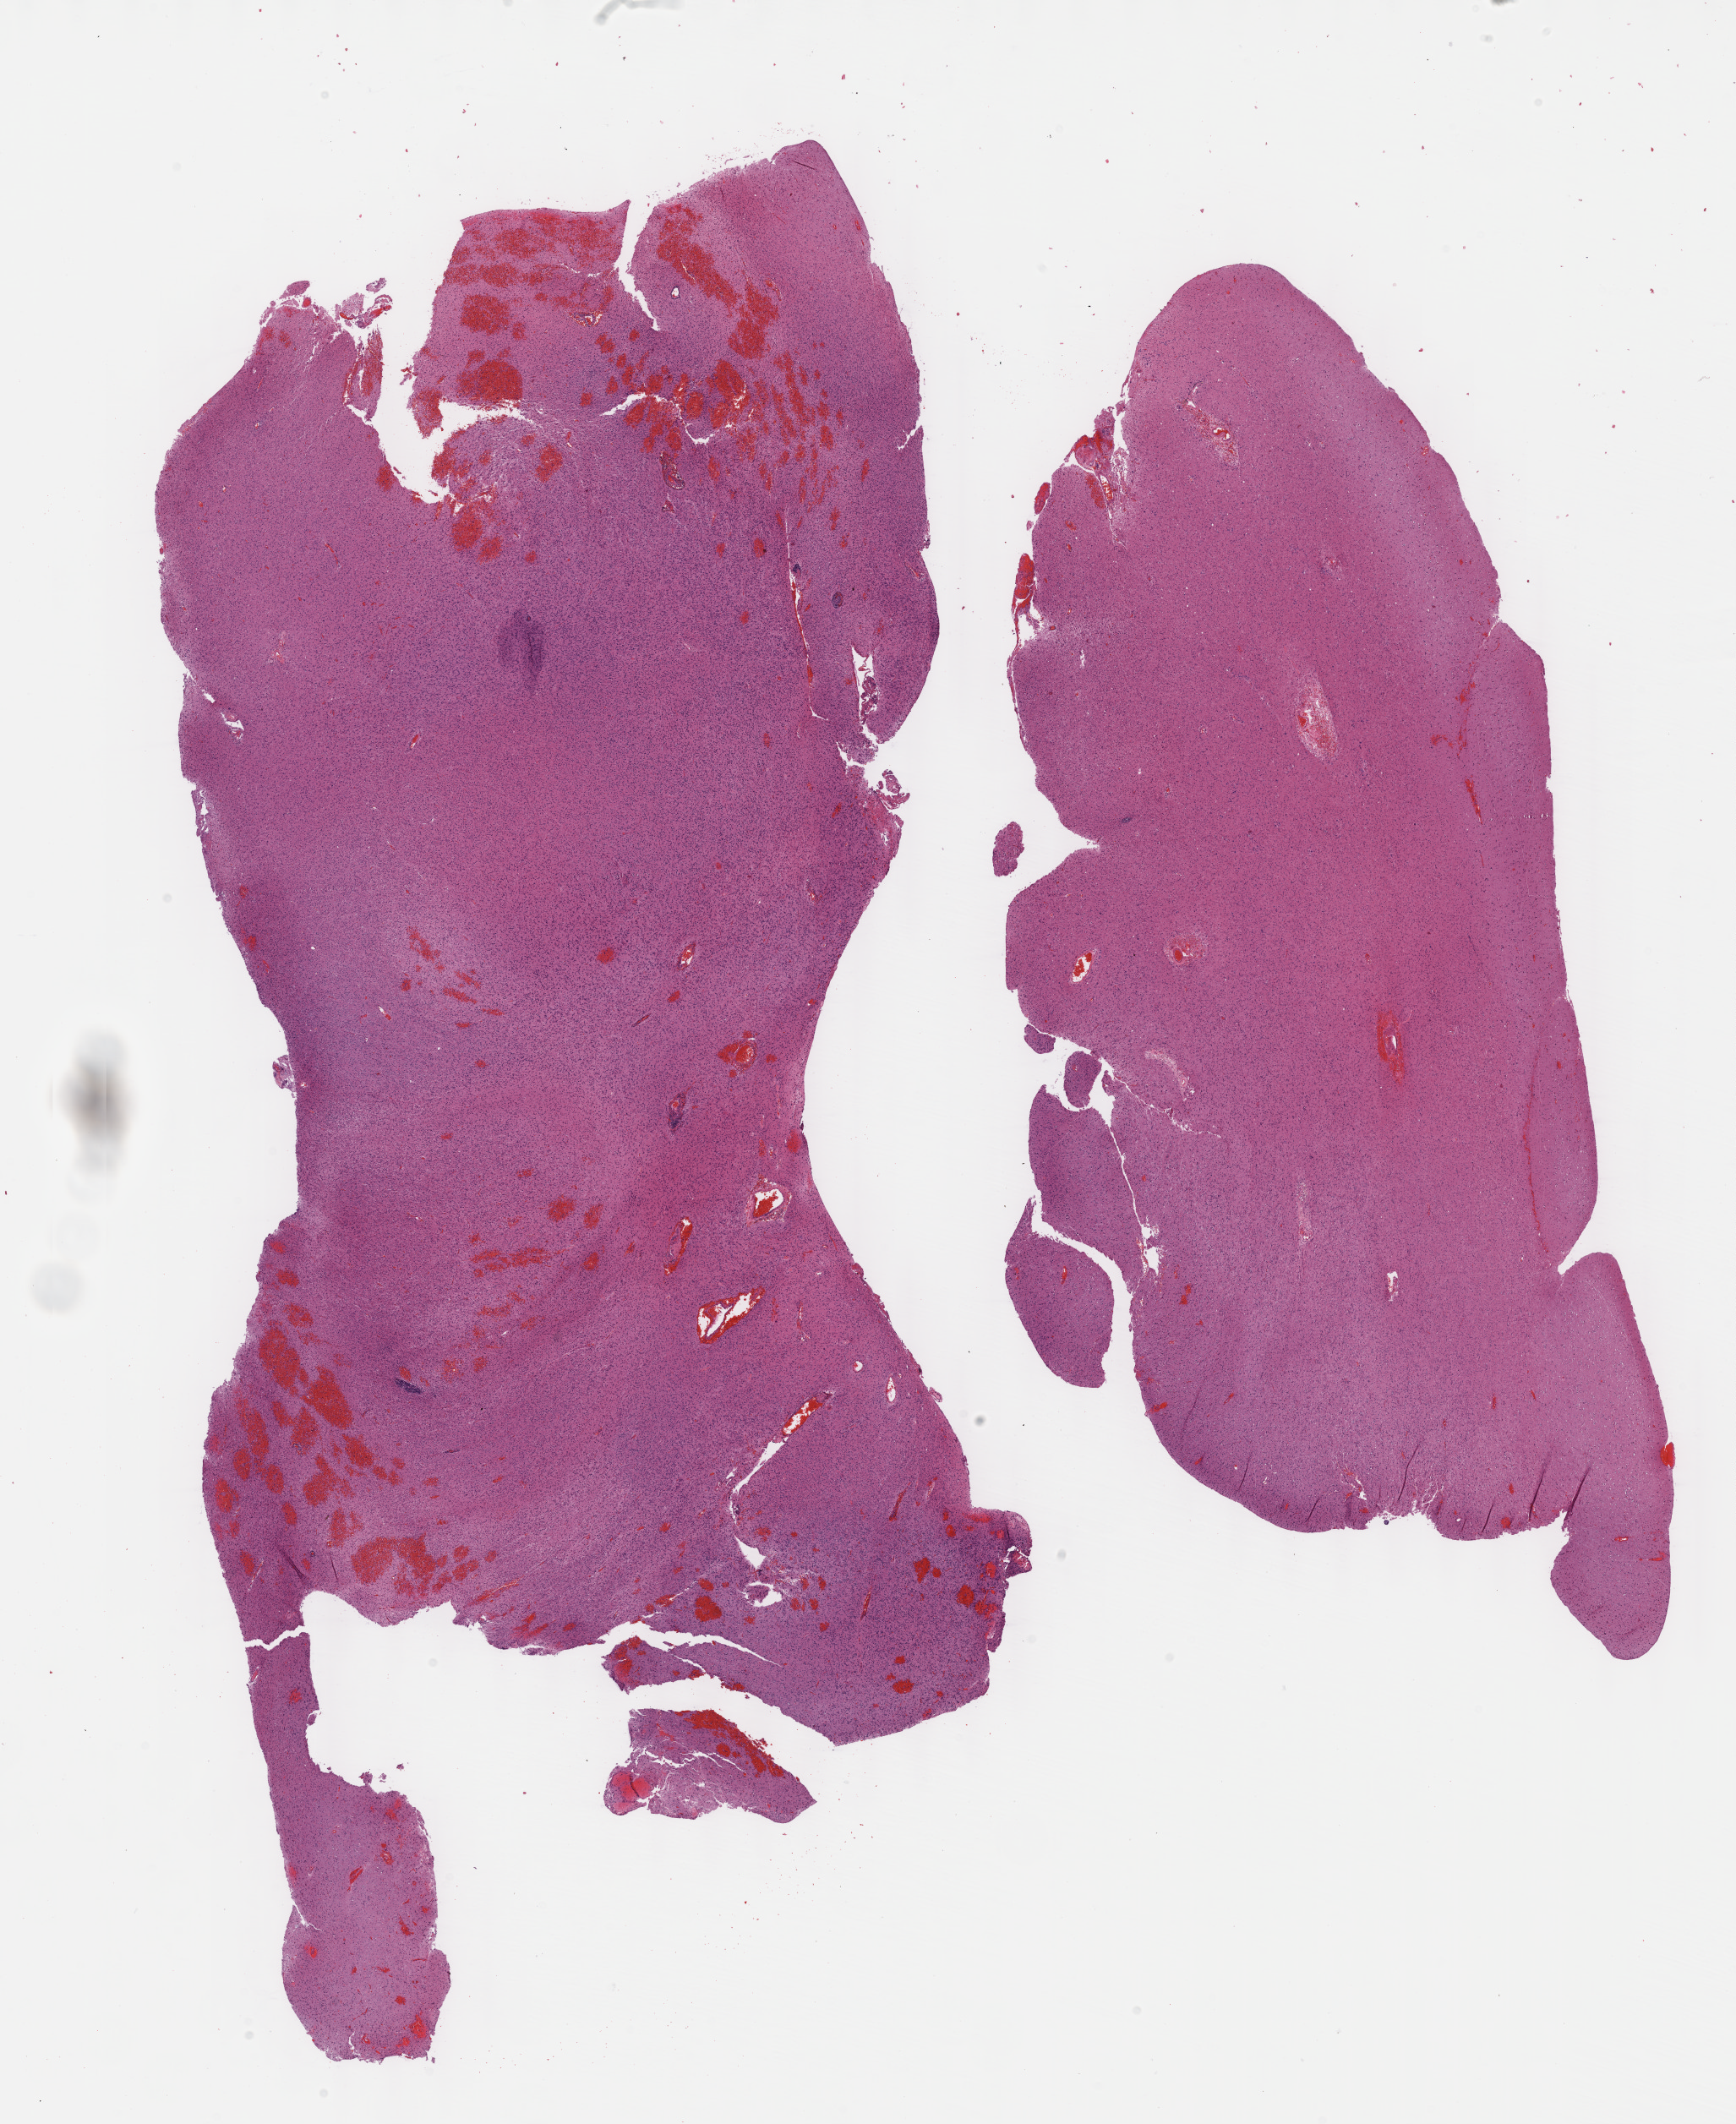
Digitized H&E tissue section (whole slide), whole scanned area (about 16.6 x 20.3 mm, acquisition: 40x scan) shown as a low-resolution overview; formalin-fixed paraffin-embedded (FFPE) diagnostic section; sample: primary tumour, brain. Patient: male, age at initial diagnosis 62 years. Histologic grade: G3 (poorly differentiated).
- histologic diagnosis: Astrocytoma, anaplastic (cerebrum)